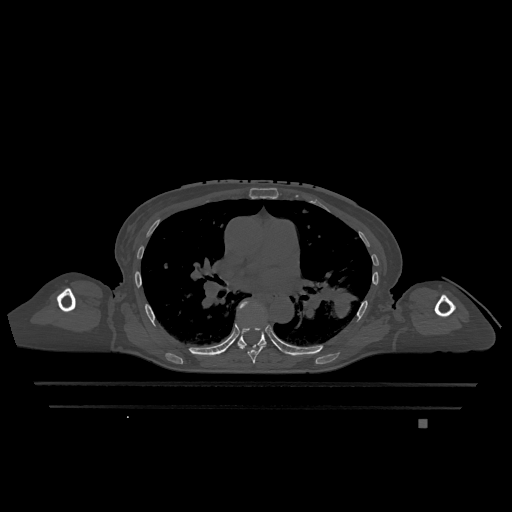
CT including the spine, one axial slice; slice 764 of 1317 in the series (ordered by position); bone window (W 1800 / L 400 HU); 512 × 512 image matrix, field of view 500 × 500 mm. Patient: female, 74 years. From the clinical record (not read from this slice): primary cancer: lung; vertebrae with lytic lesions (as recorded): T1, T4, T5, T6, L4, L5.
Structures marked on this image (semi-automatic segmentation, software-assisted and operator-edited):
- T6 vertebra: box from (x=239, y=345) to (x=265, y=363) px
- T7 vertebra: (x=237, y=301)–(x=267, y=348)